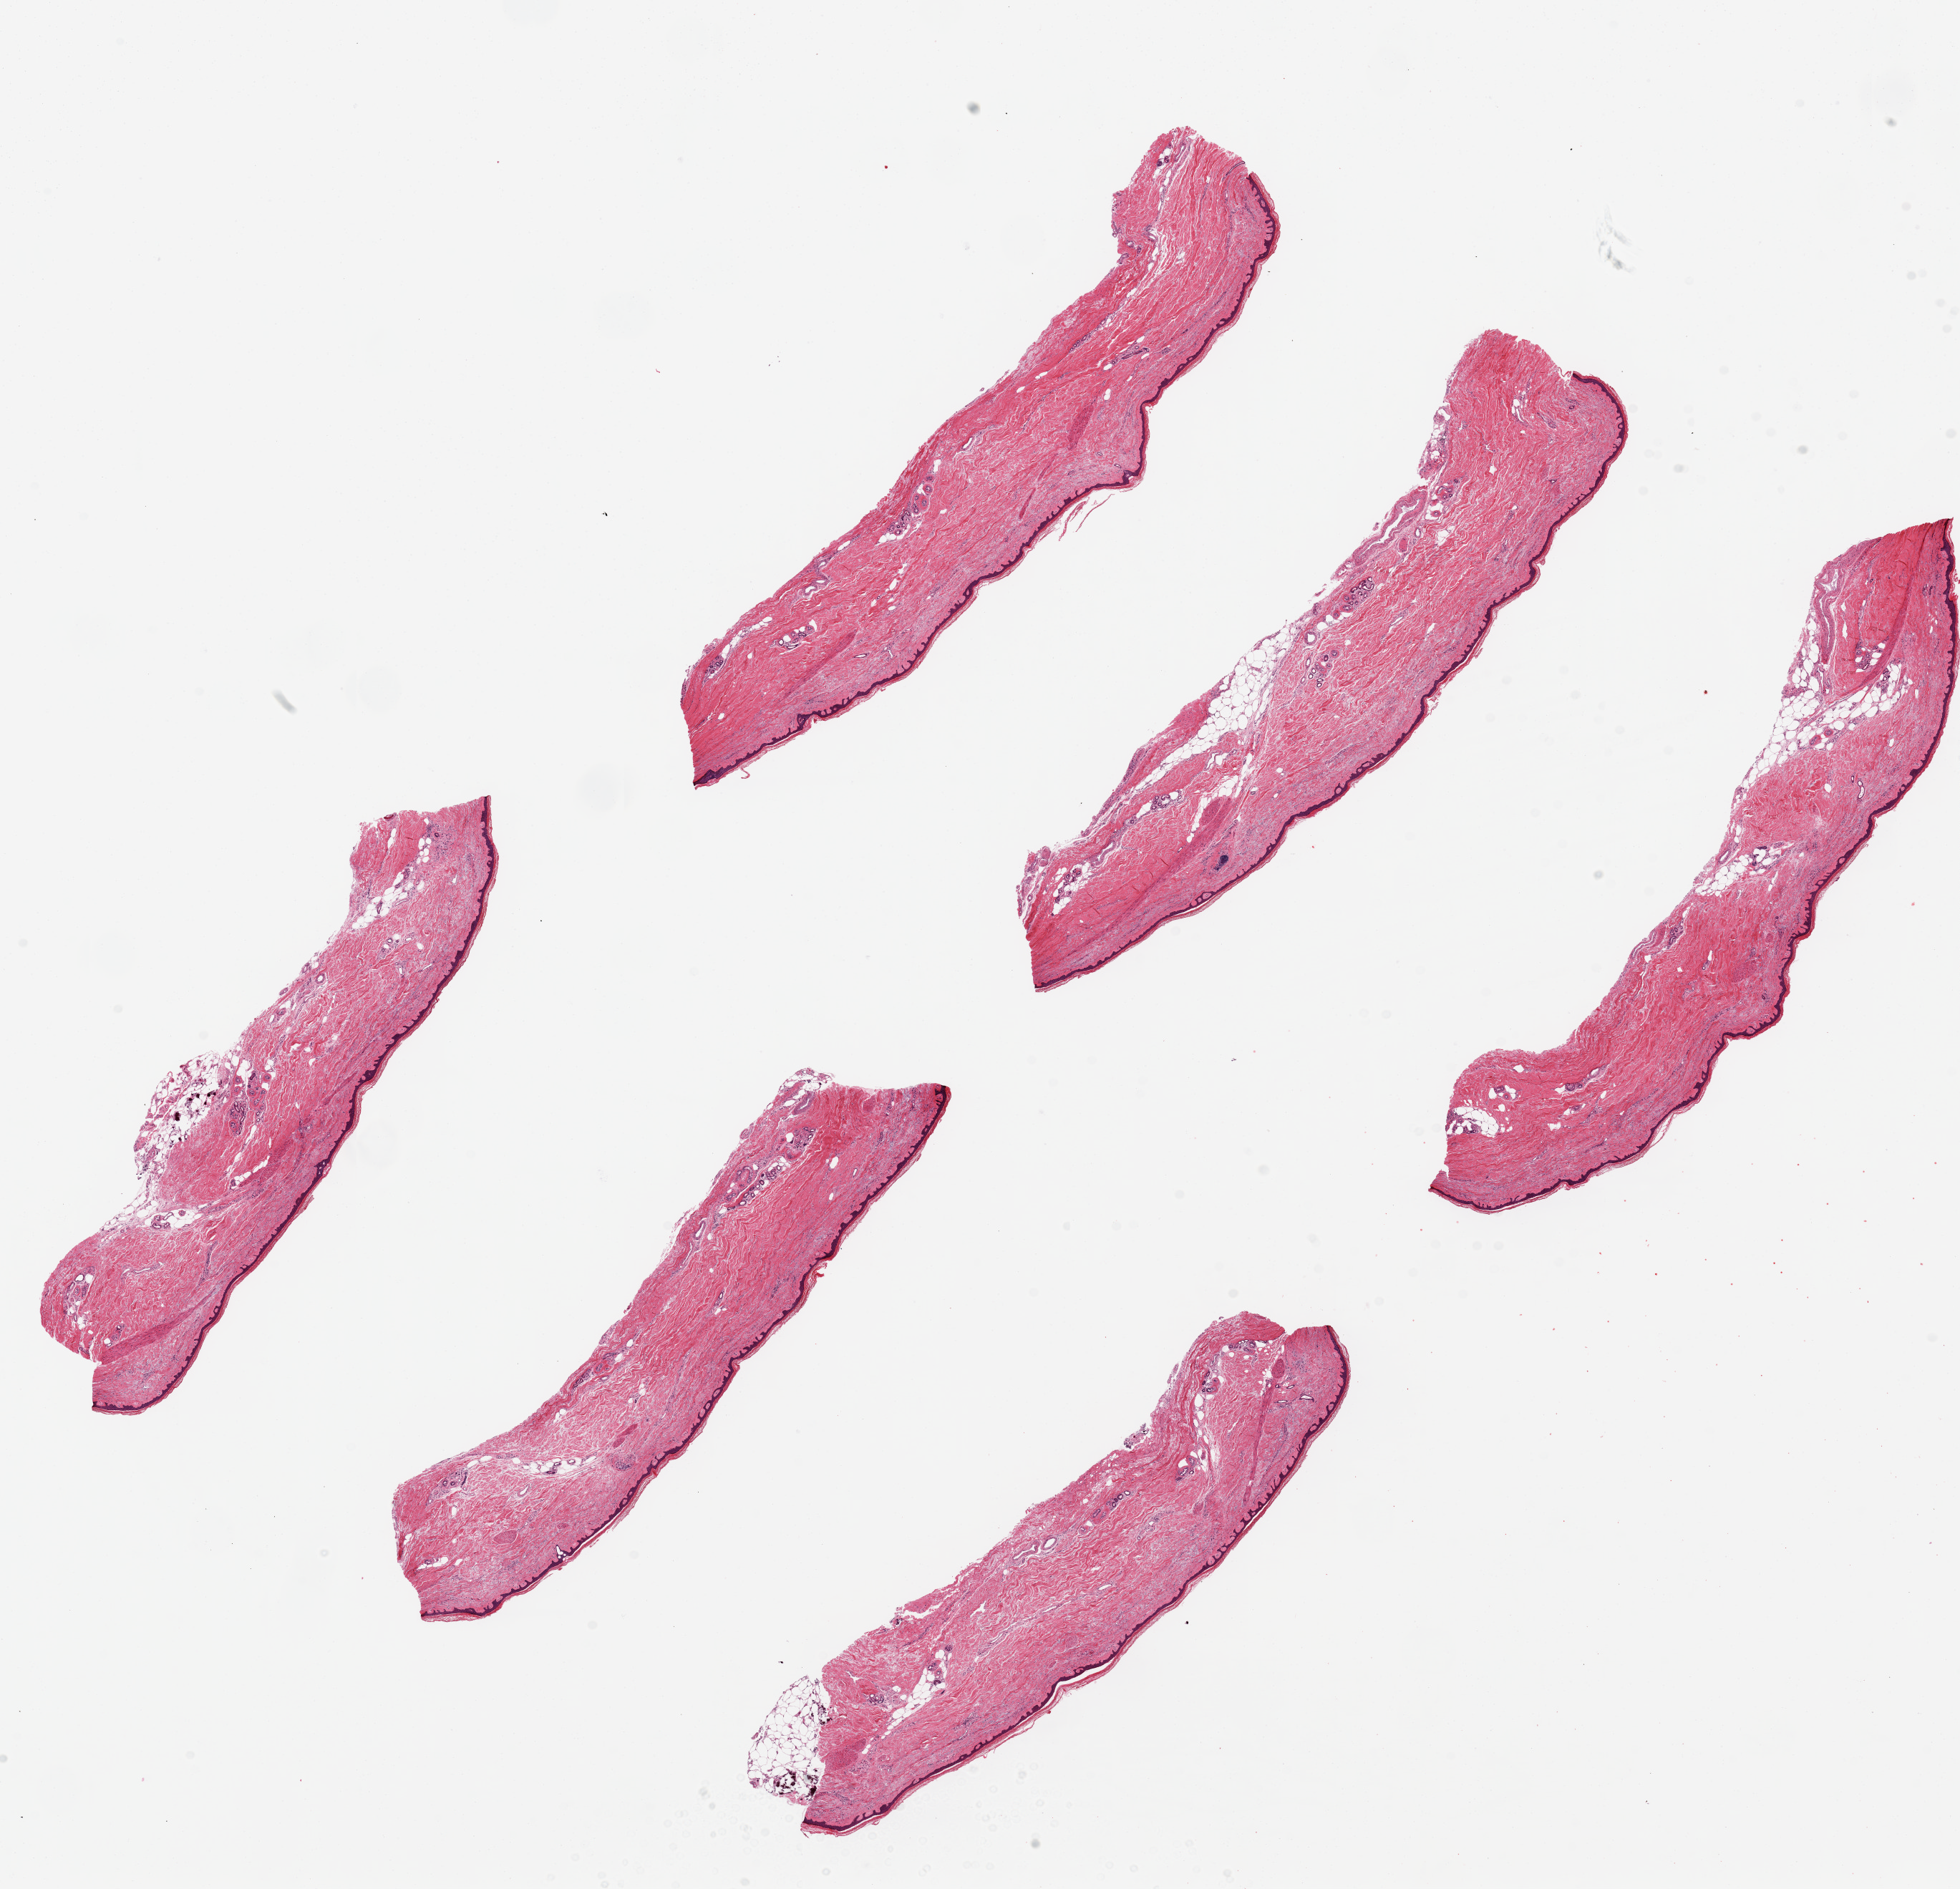
Hematoxylin and eosin (H&E) whole-slide image, shown as a low-resolution overview of the whole scanned area (about 21.7 x 20.9 mm); PAXgene-fixed paraffin-embedded (PFPE) section; sampled site (target tissue): skin of lower leg; donor tissue sample. Donor: female.
• pathologist's review note for this sample: 6 ~8x1.5mm pieces. Squamous epithelium is ~2-3% of thickness